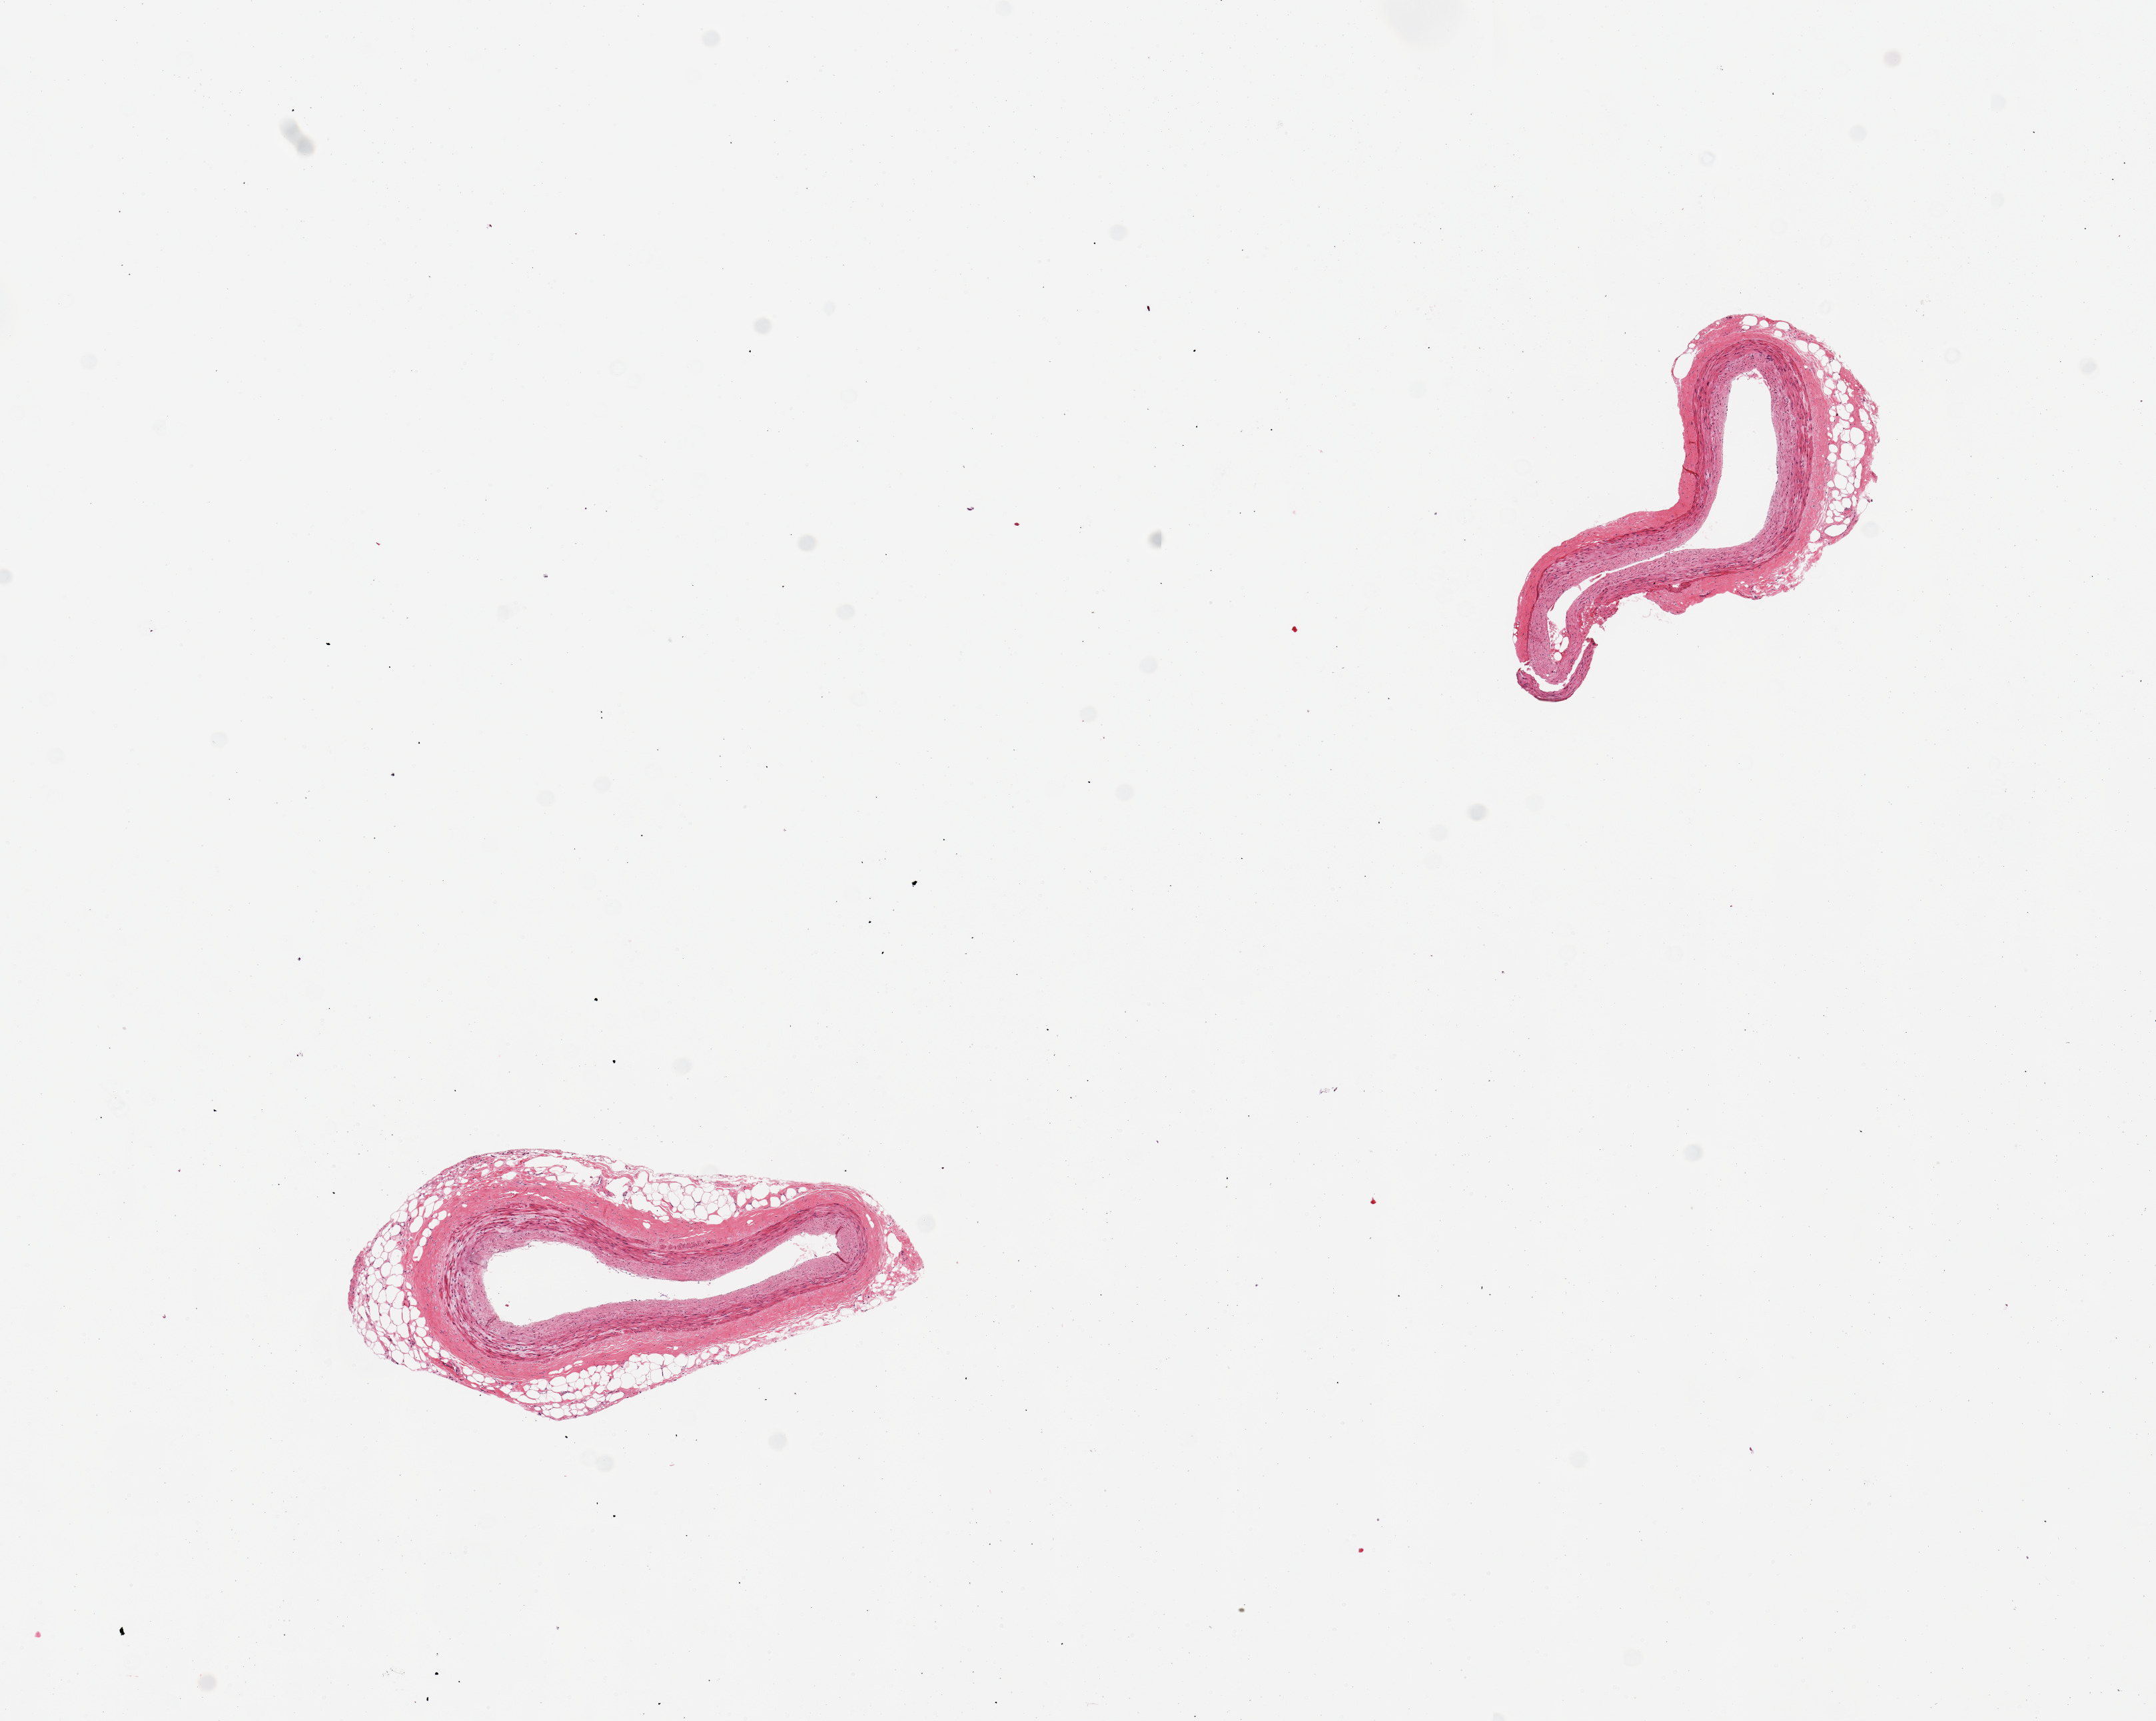
Digitized haematoxylin and eosin-stained section, a low-resolution overview of the entire scanned area, about 12.8 x 10.2 mm, PAXgene-fixed, paraffin-embedded tissue, section of coronary artery (target tissue), donor tissue sample.
• review note (as recorded): 2 pieces, minimal atherosis, discontinuous rim of fat, ~0.3mm